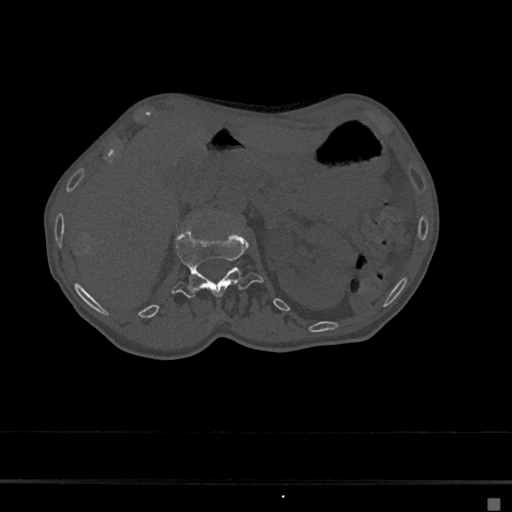
CT including the spine, one axial slice; position 70 of 797 along the scan axis; reconstruction kernel Br40s/3; bone window (W 1800 / L 400 HU); 0.5 mm slice thickness; 512 × 512 image matrix. Patient: female, 68 years. From the clinical record (not read from this slice): primary cancer: renal.
Annotated regions visible in this slice (semi-automatically segmented with operator editing):
- L1 vertebra: box from (x=172, y=226) to (x=264, y=299) px